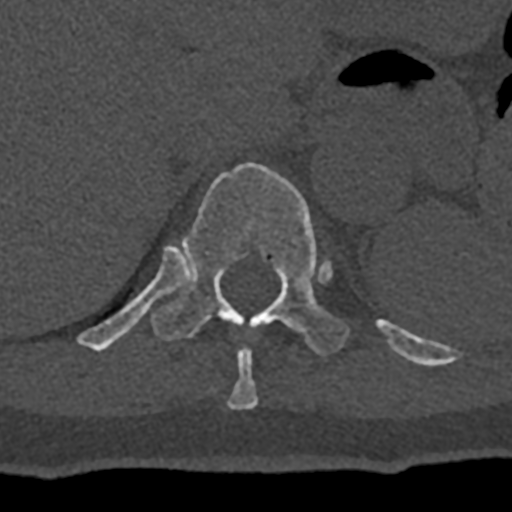
CT including the spine, one axial slice. Position 557 of 797 along the scan axis. Reconstruction kernel Br40s/3. 120 kVp. Bone window (W 1800 / L 400 HU). 0.5 mm slice thickness. 512 × 512 image matrix, field of view 160 × 160 mm. Male patient, age 74 years. From the clinical record (not read from this slice): primary cancer: renal.
Outlined on this slice (semi-automatically segmented with operator editing):
- T10 vertebra: bounding box (x1, y1, x2, y2) in pixels: (227, 348, 258, 409)
- T11 vertebra: (77, 163, 432, 367)